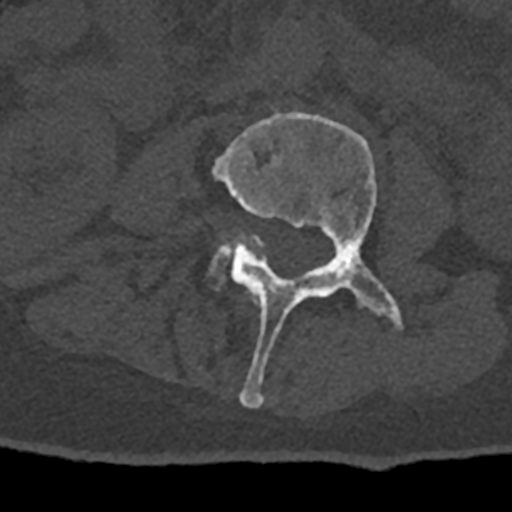
CT including the spine, one axial slice. Slice 312 of 797 in the series (ordered by position). Reconstruction kernel Br40s/3. 120 kVp. Bone window (W 1800 / L 400 HU). 0.5 mm slice thickness. 512 × 512 image matrix. Patient: male, 74 years. Case-level facts recorded for this patient, not image findings: primary cancer: renal; vertebrae with lytic lesions (as recorded): T10, L1, L2, L3, L4, L5.
Structures marked on this image (semi-automatic segmentation, software-assisted and operator-edited):
- L3 vertebra: bounding box (x1, y1, x2, y2) in pixels: (213, 110, 404, 408)
- L4 vertebra: (210, 236, 263, 286)